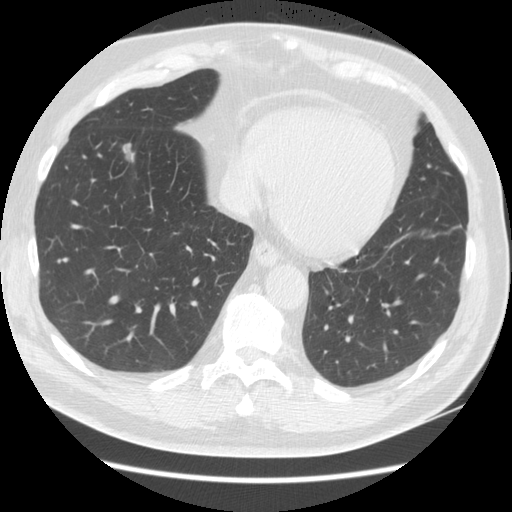
Low-dose screening chest CT, one axial slice. Reconstruction kernel STANDARD. 140 kVp. Lung window (W 1500 / L -600 HU). 2.5 mm slice thickness. 512 × 512 image matrix, field of view 360 × 360 mm.
Annotated regions visible in this slice (manually delineated by an expert):
- lesion 1 (tumor, lower lobe of right lung): box from (x=123, y=143) to (x=135, y=162) px